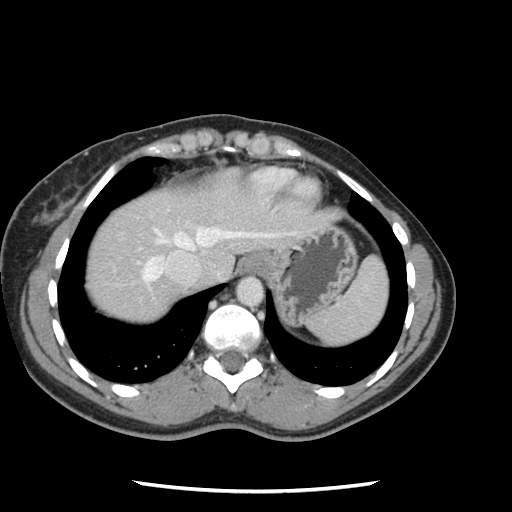
Contrast-enhanced abdominal CT, one axial slice; position 106 of 134 along the scan axis; 120 kVp; intravenous contrast given; soft-tissue window (W 400 / L 40 HU); 512 × 512 image matrix, field of view 330 × 330 mm. Female patient, age 43 years. Case-level facts recorded for this patient, not image findings: diagnosis: colorectal cancer liver metastases, imaged before liver resection; multiple liver metastases: yes; largest metastasis: 3.4 cm; chemotherapy before resection: no.
Structures marked on this image (expert manual segmentation):
- hepatic veins: bounding box [x1, y1, x2, y2] px = [142, 227, 275, 282]
- liver: [86, 191, 301, 321]
- planned liver remnant (the part of the liver to remain after resection): [86, 193, 202, 301]
- portal vein (with intrahepatic branches): [139, 247, 143, 250]